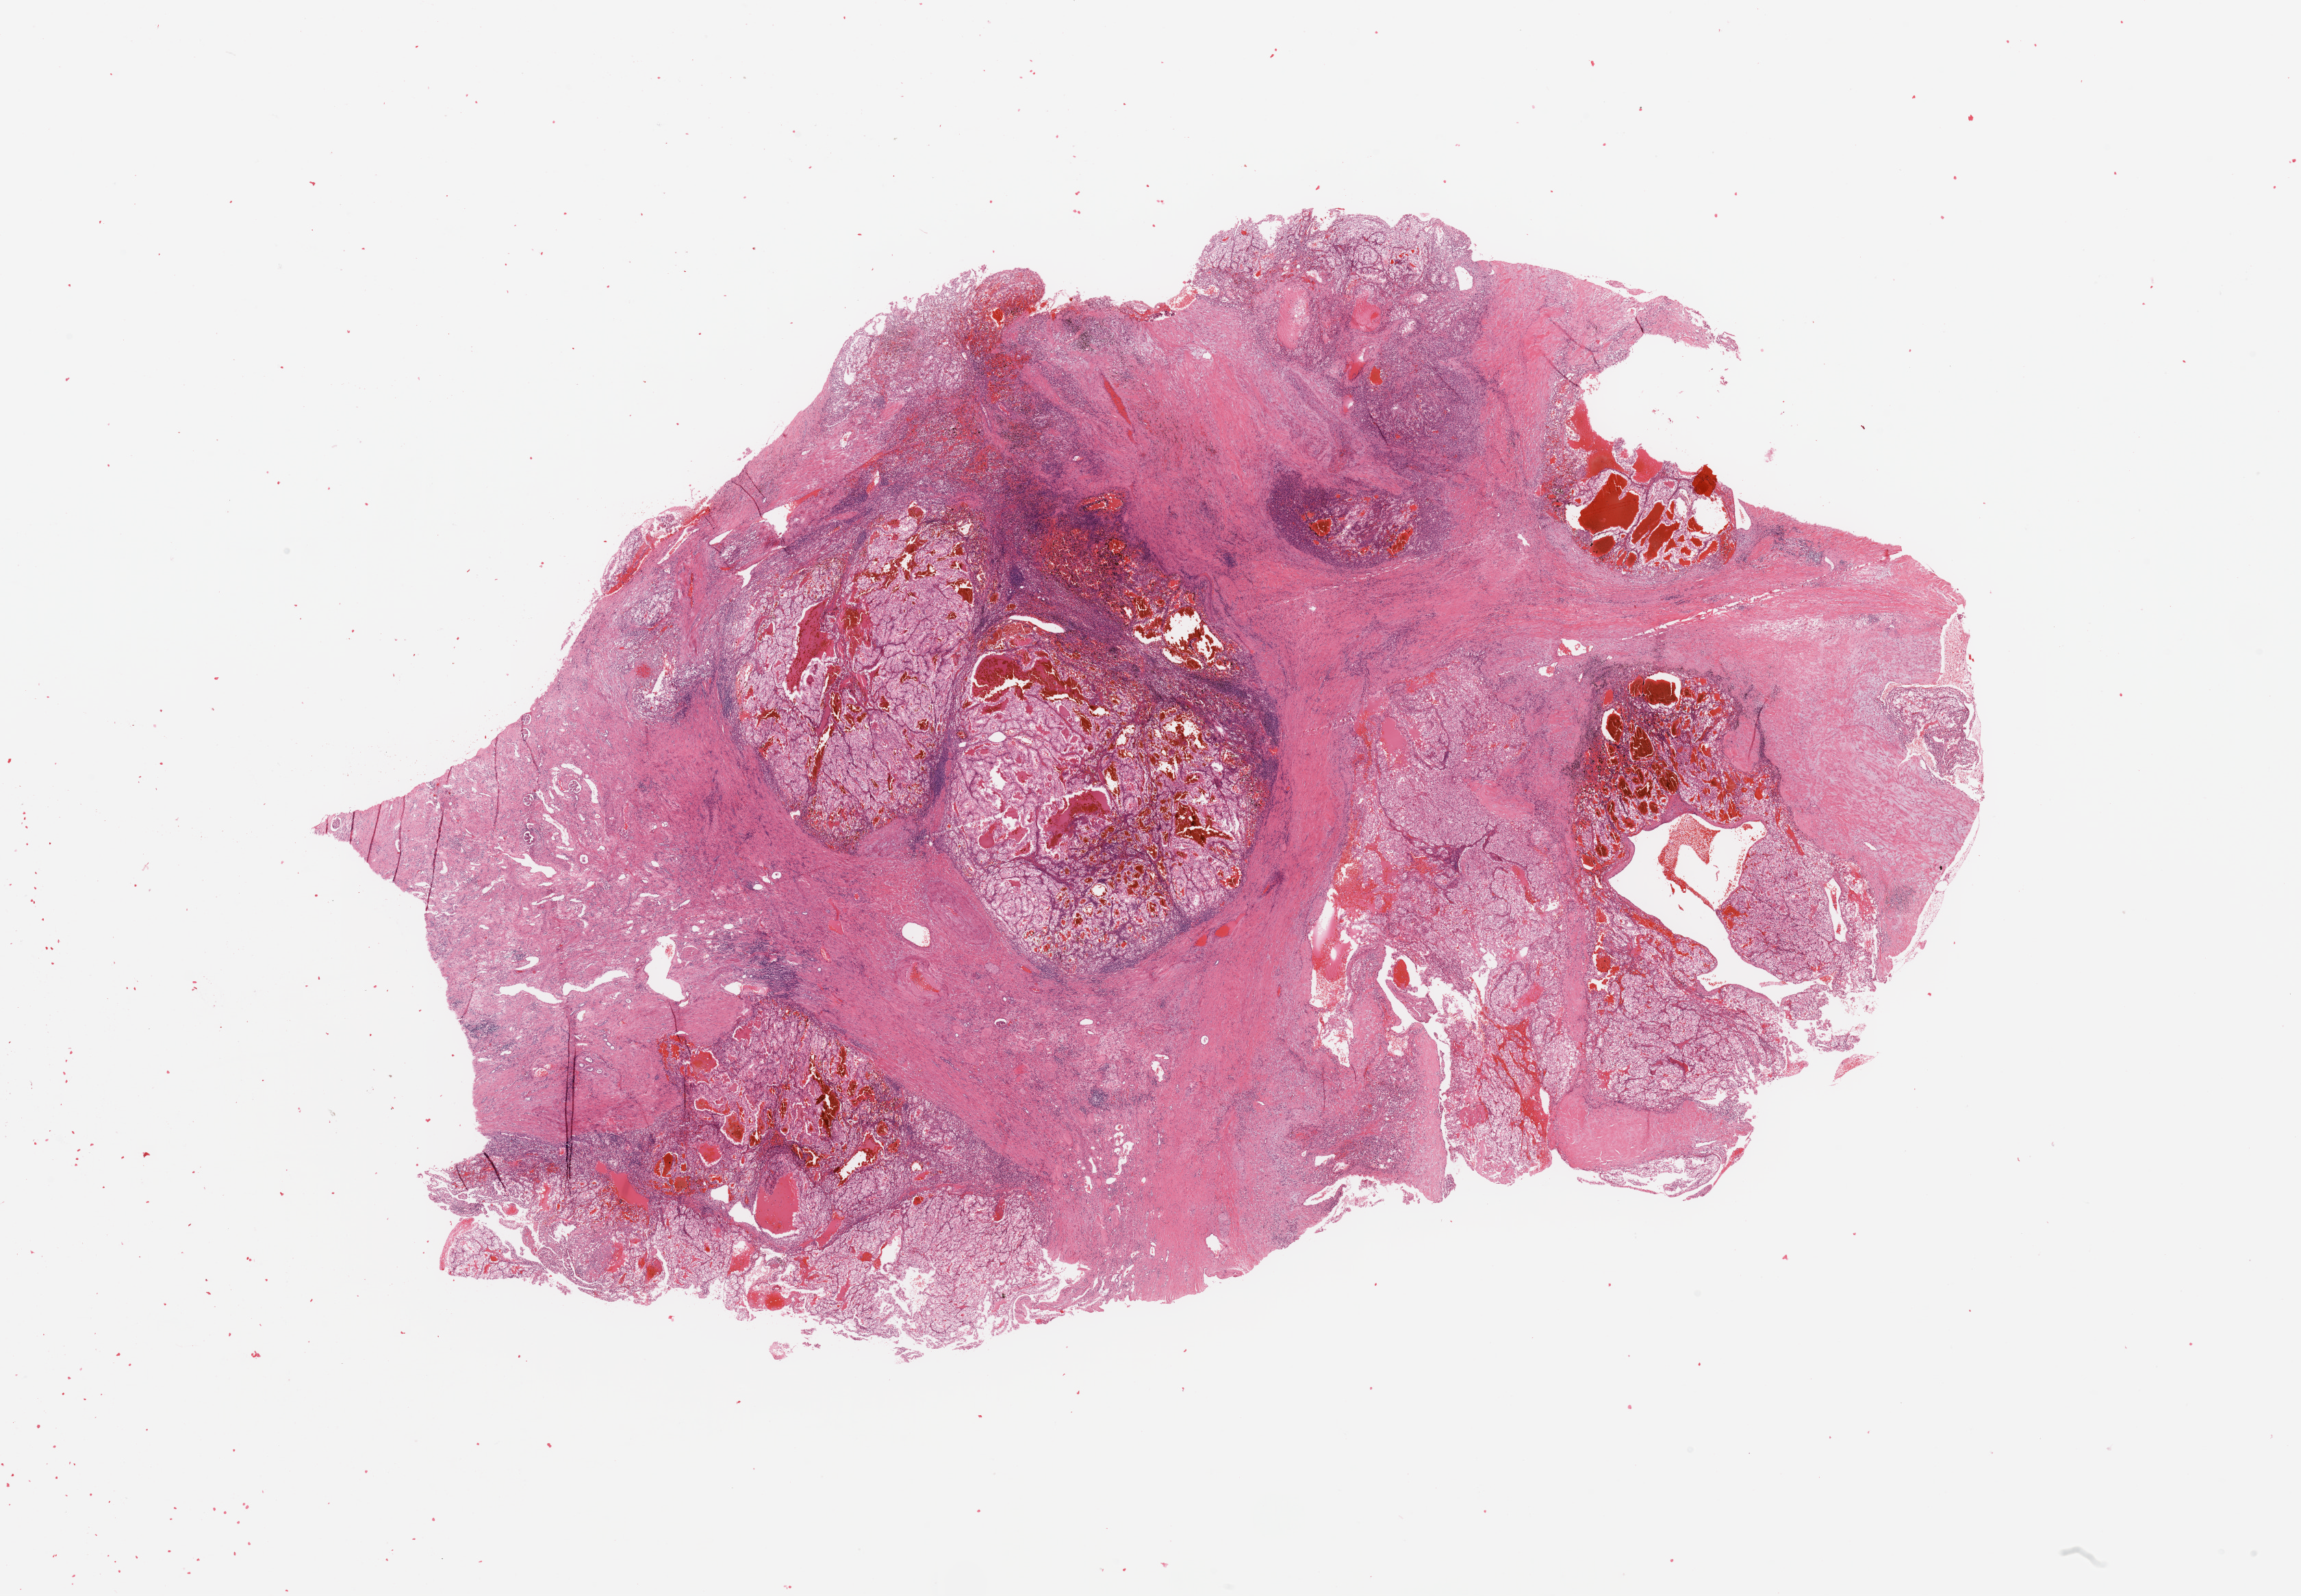
H&E whole-slide image — whole scanned area (about 26.6 x 18.4 mm, slide scanned at 20x) shown as a low-resolution overview; tumour tissue sample, kidney. Female, 54 y/o. Histologic grade: G2 (moderately differentiated).
Histologic diagnosis: Renal cell carcinoma, NOS.